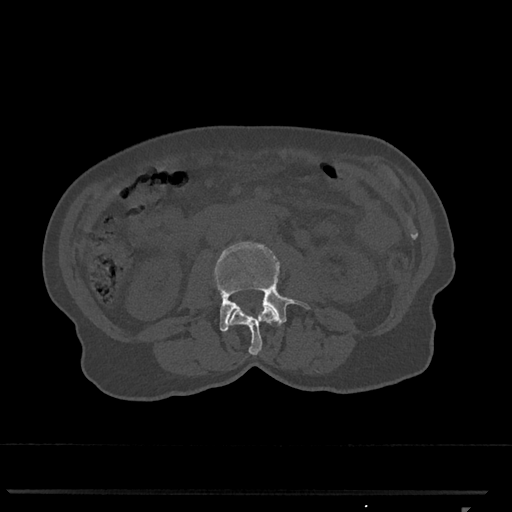
CT including the spine, one axial slice; position 297 of 793 along the scan axis; reconstruction kernel Br40s/3; bone window (W 1800 / L 400 HU); 512 × 512 image matrix, field of view 380 × 380 mm. Female patient, age 62 years. Case-level facts recorded for this patient, not image findings: primary cancer: renal.
Outlined on this slice (semi-automatically segmented with operator editing):
- L2 vertebra: bounding box [x1, y1, x2, y2] px = [228, 306, 278, 355]
- L3 vertebra: [214, 242, 310, 332]